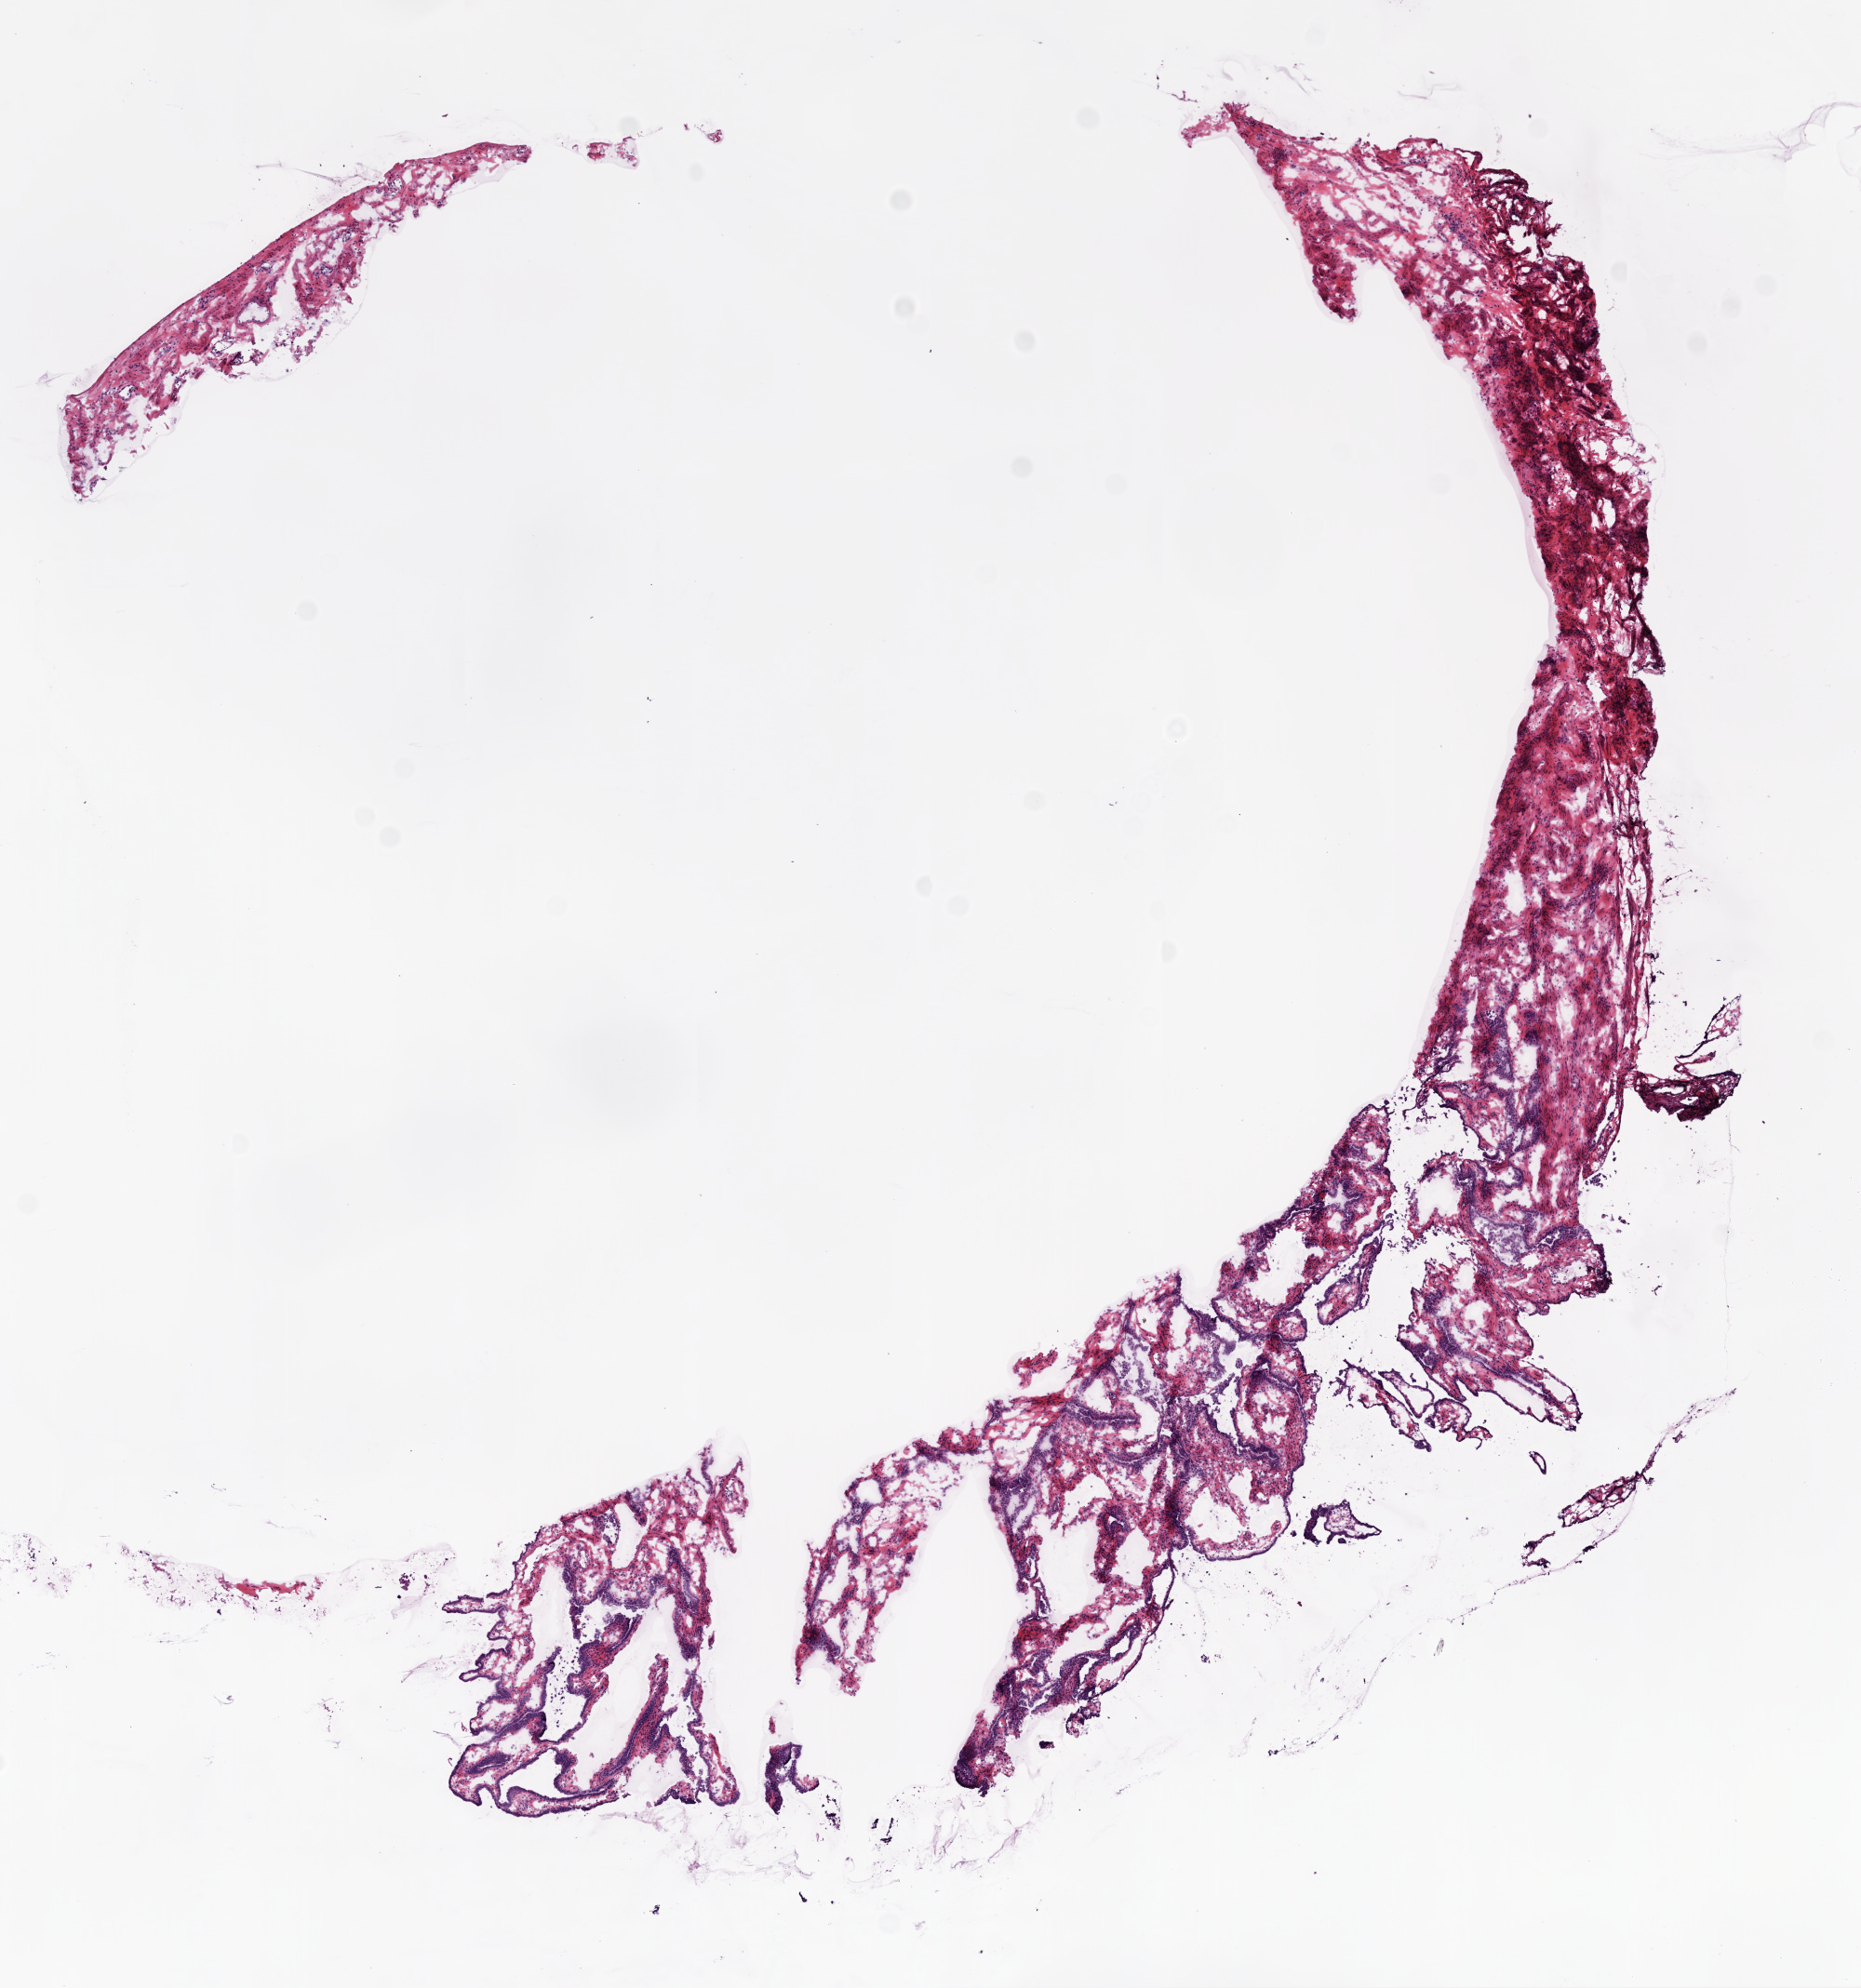
H&E-stained whole-slide image — a low-resolution overview of the entire scanned area, about 8.0 x 8.6 mm (from a 20x scan). Frozen section from the bottom of the tissue portion. Ovary, solid tissue normal (non-tumour tissue) sample. Patient: female, age at initial diagnosis 63 years.
This section: solid tissue normal (non-tumour) sample from the same patient. Patient diagnosis: Serous cystadenocarcinoma, NOS.